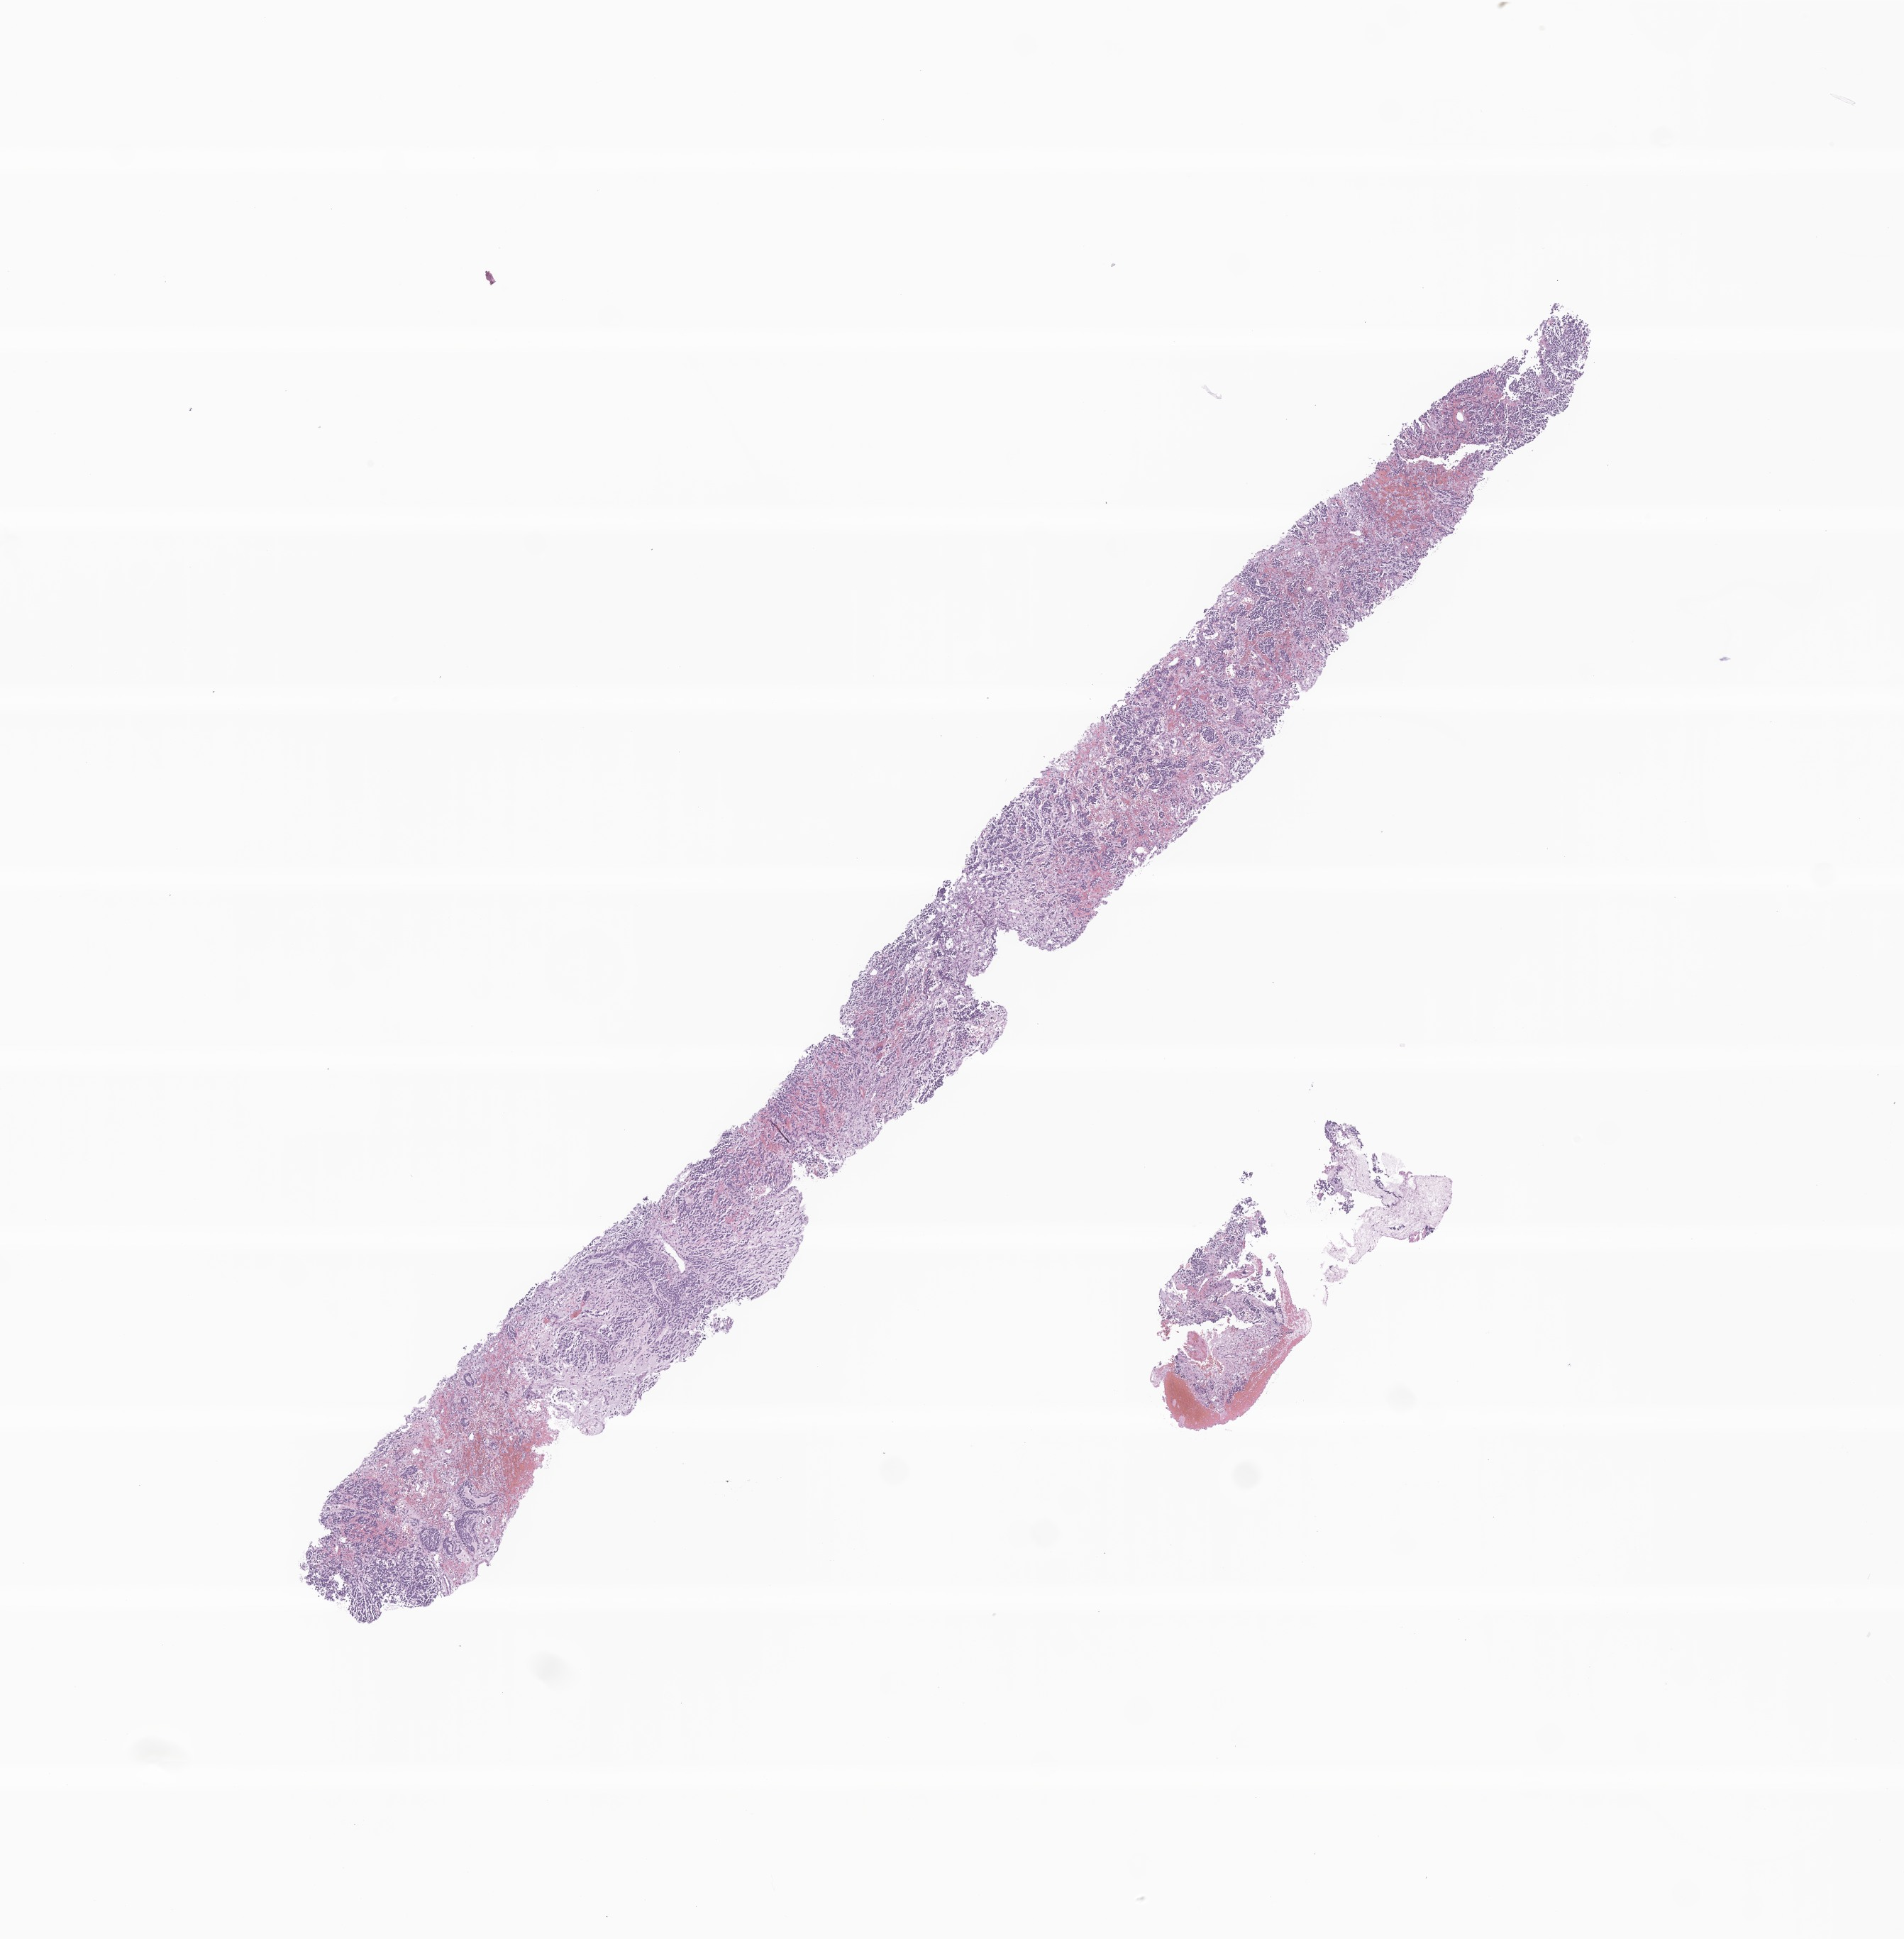
Haematoxylin and eosin whole-slide image of tumor tissue from the adrenal gland — whole scanned area (about 11.3 x 11.5 mm) shown as a low-resolution overview, formalin-fixed paraffin-embedded section. Patient male; age 585 days (about 1.6 years).
Diagnosis: Neuroblastoma, NOS.